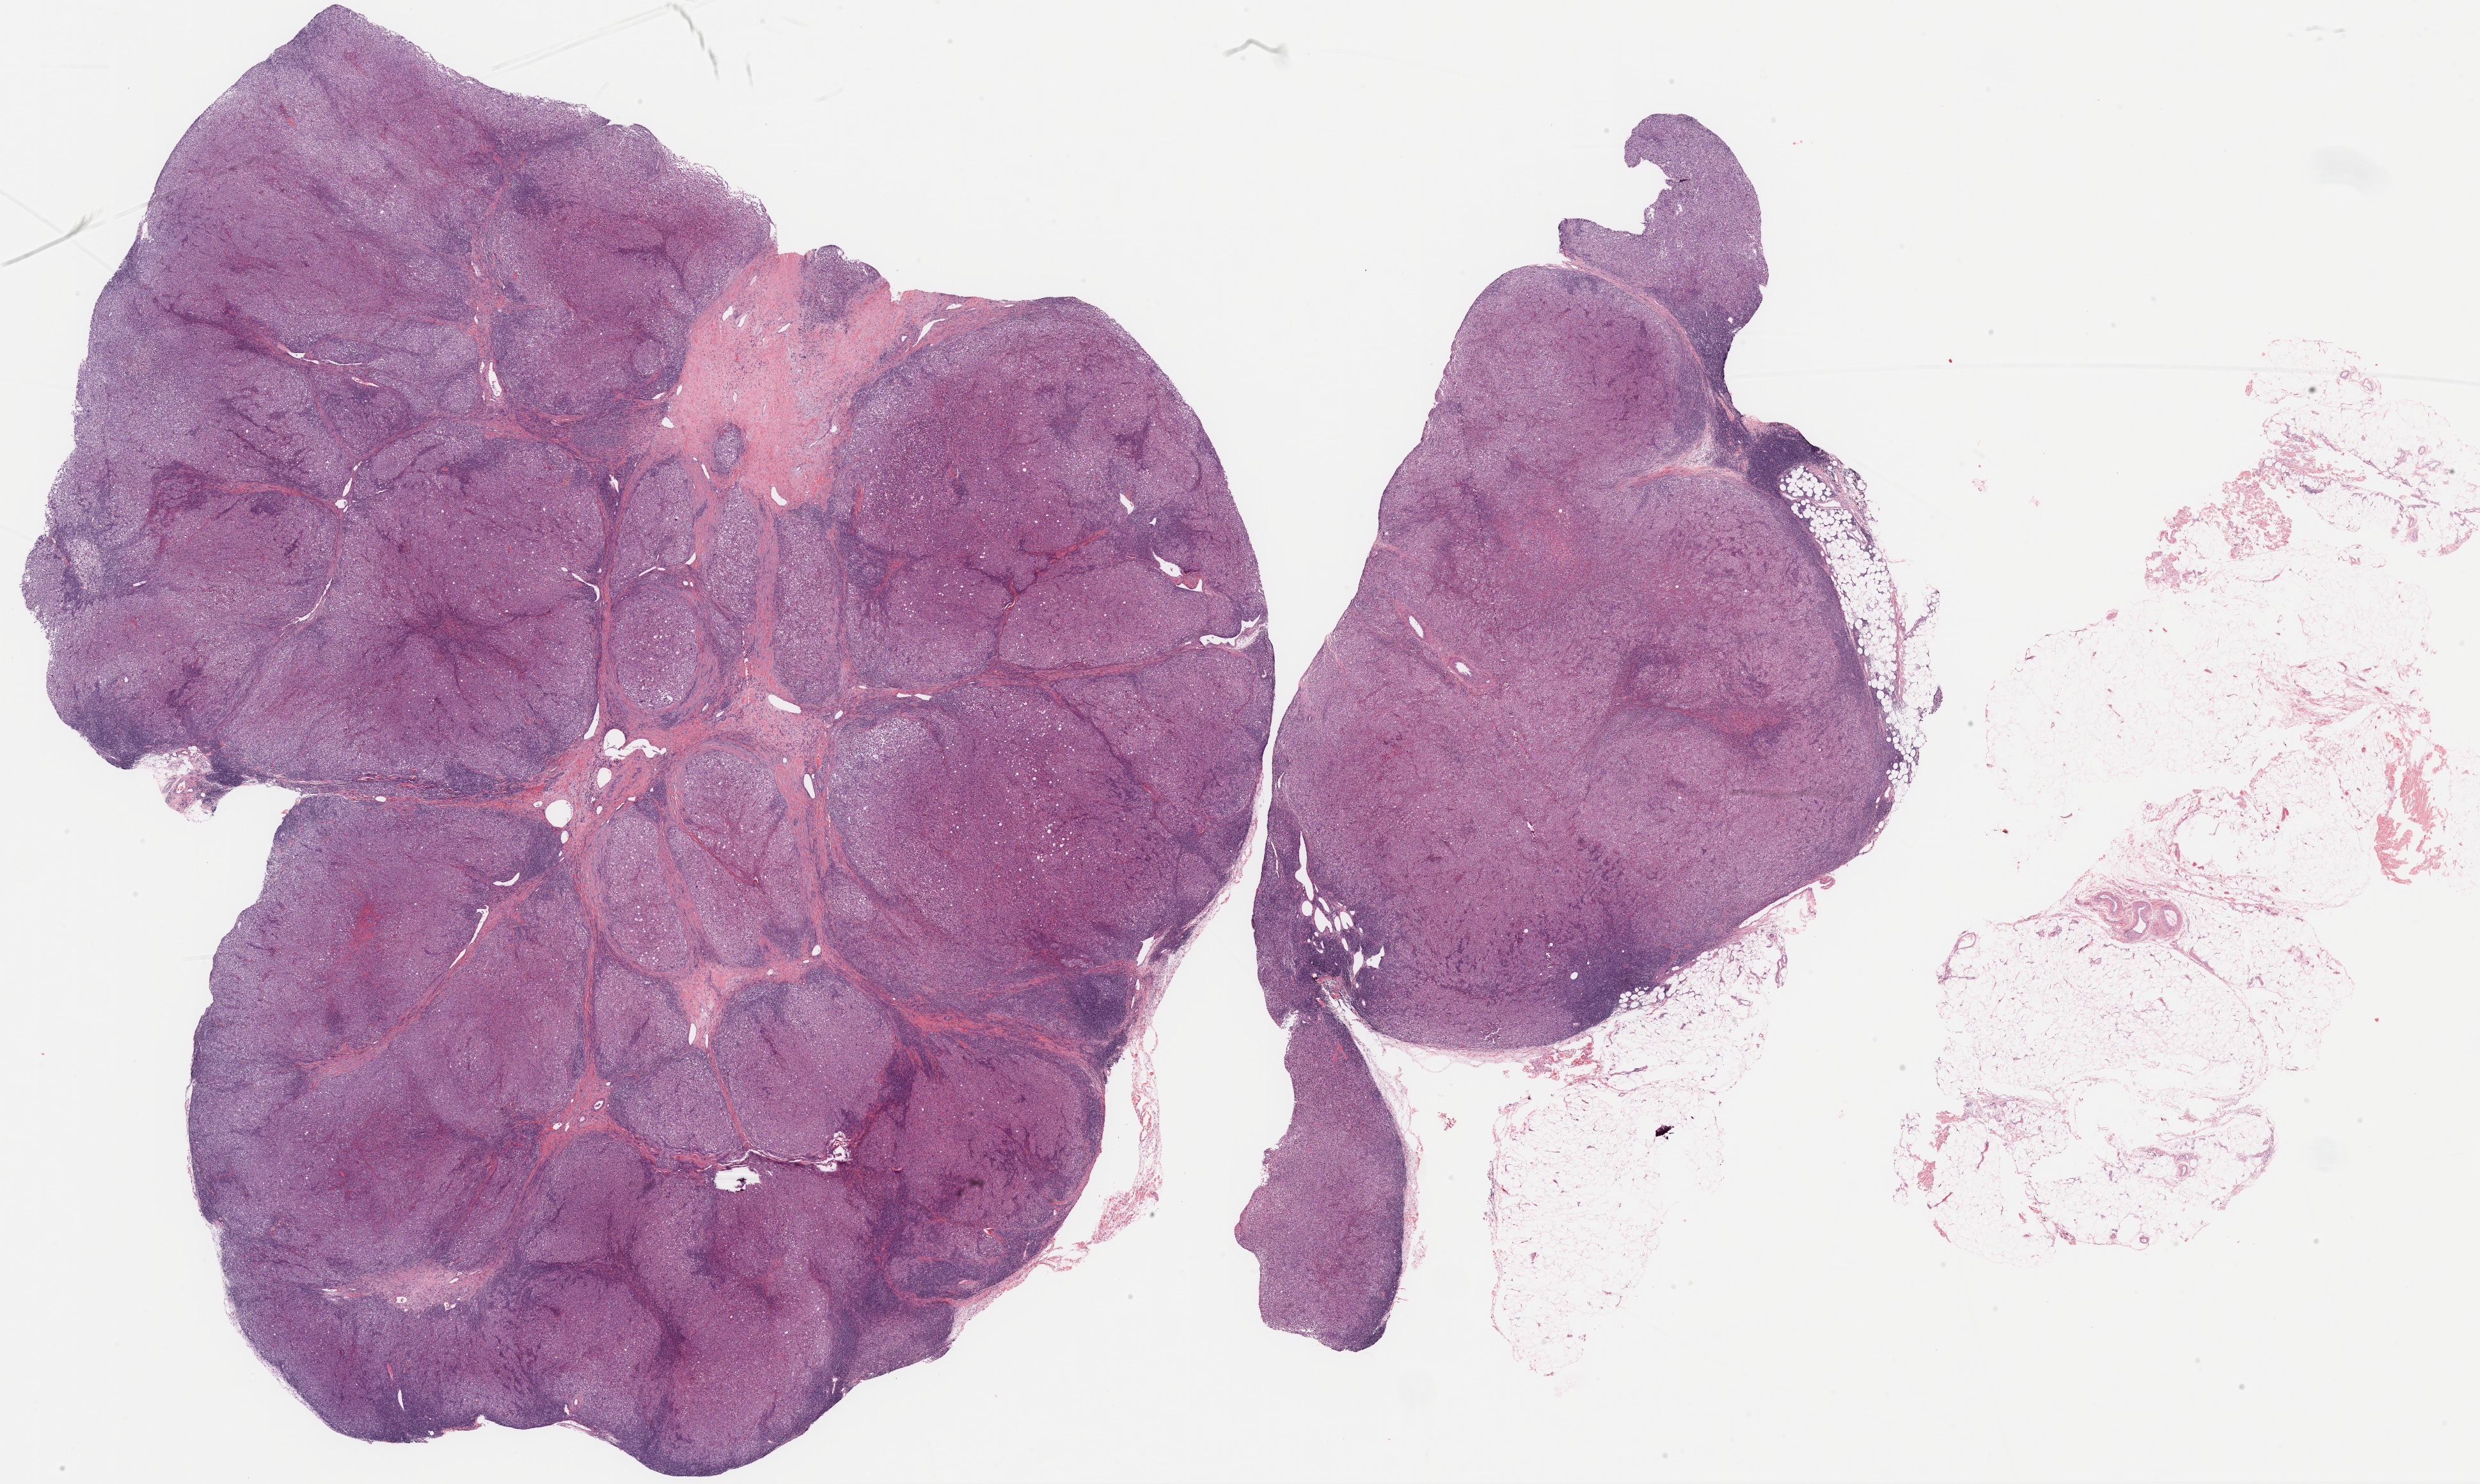
Digitized H&E tissue section (whole slide) — shown as a low-resolution overview of the whole scanned area (about 31.3 x 18.7 mm); formalin-fixed paraffin-embedded (FFPE) diagnostic section; metastatic tumour sample, sampled site: lymph nodes of inguinal region or leg. Male, age 51 years at initial diagnosis.
* this section: metastatic tumour tissue
* patient diagnosis: Nodular melanoma